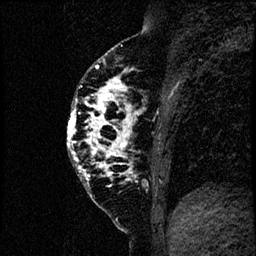
Breast MRI (dynamic contrast-enhanced), one sagittal slice; position 30 of 60 along the scan axis; dynamic contrast-enhanced study with each time point stored as its own series, time point 2 of 4 at this slice position (early post-contrast, ordered by acquisition time); 1.5 T; TE 4.2 ms, TR 17.6 ms; 256 × 256 image matrix. Patient: female, 40 years. From the clinical record (not read from this slice): setting: breast cancer imaged before/during neoadjuvant chemotherapy; receptor status: HER2-positive.
Structures marked on this image (semi-automatic segmentation, software-assisted and operator-edited):
- analysis volume of interest (the breast-tissue region the enhancement analysis was run in; not a lesion): box from (x=66, y=55) to (x=185, y=206) px
- tumour enhancement mask (voxels above the 100 % enhancement threshold inside the analysis volume of interest): (x=67, y=65)–(x=141, y=179)